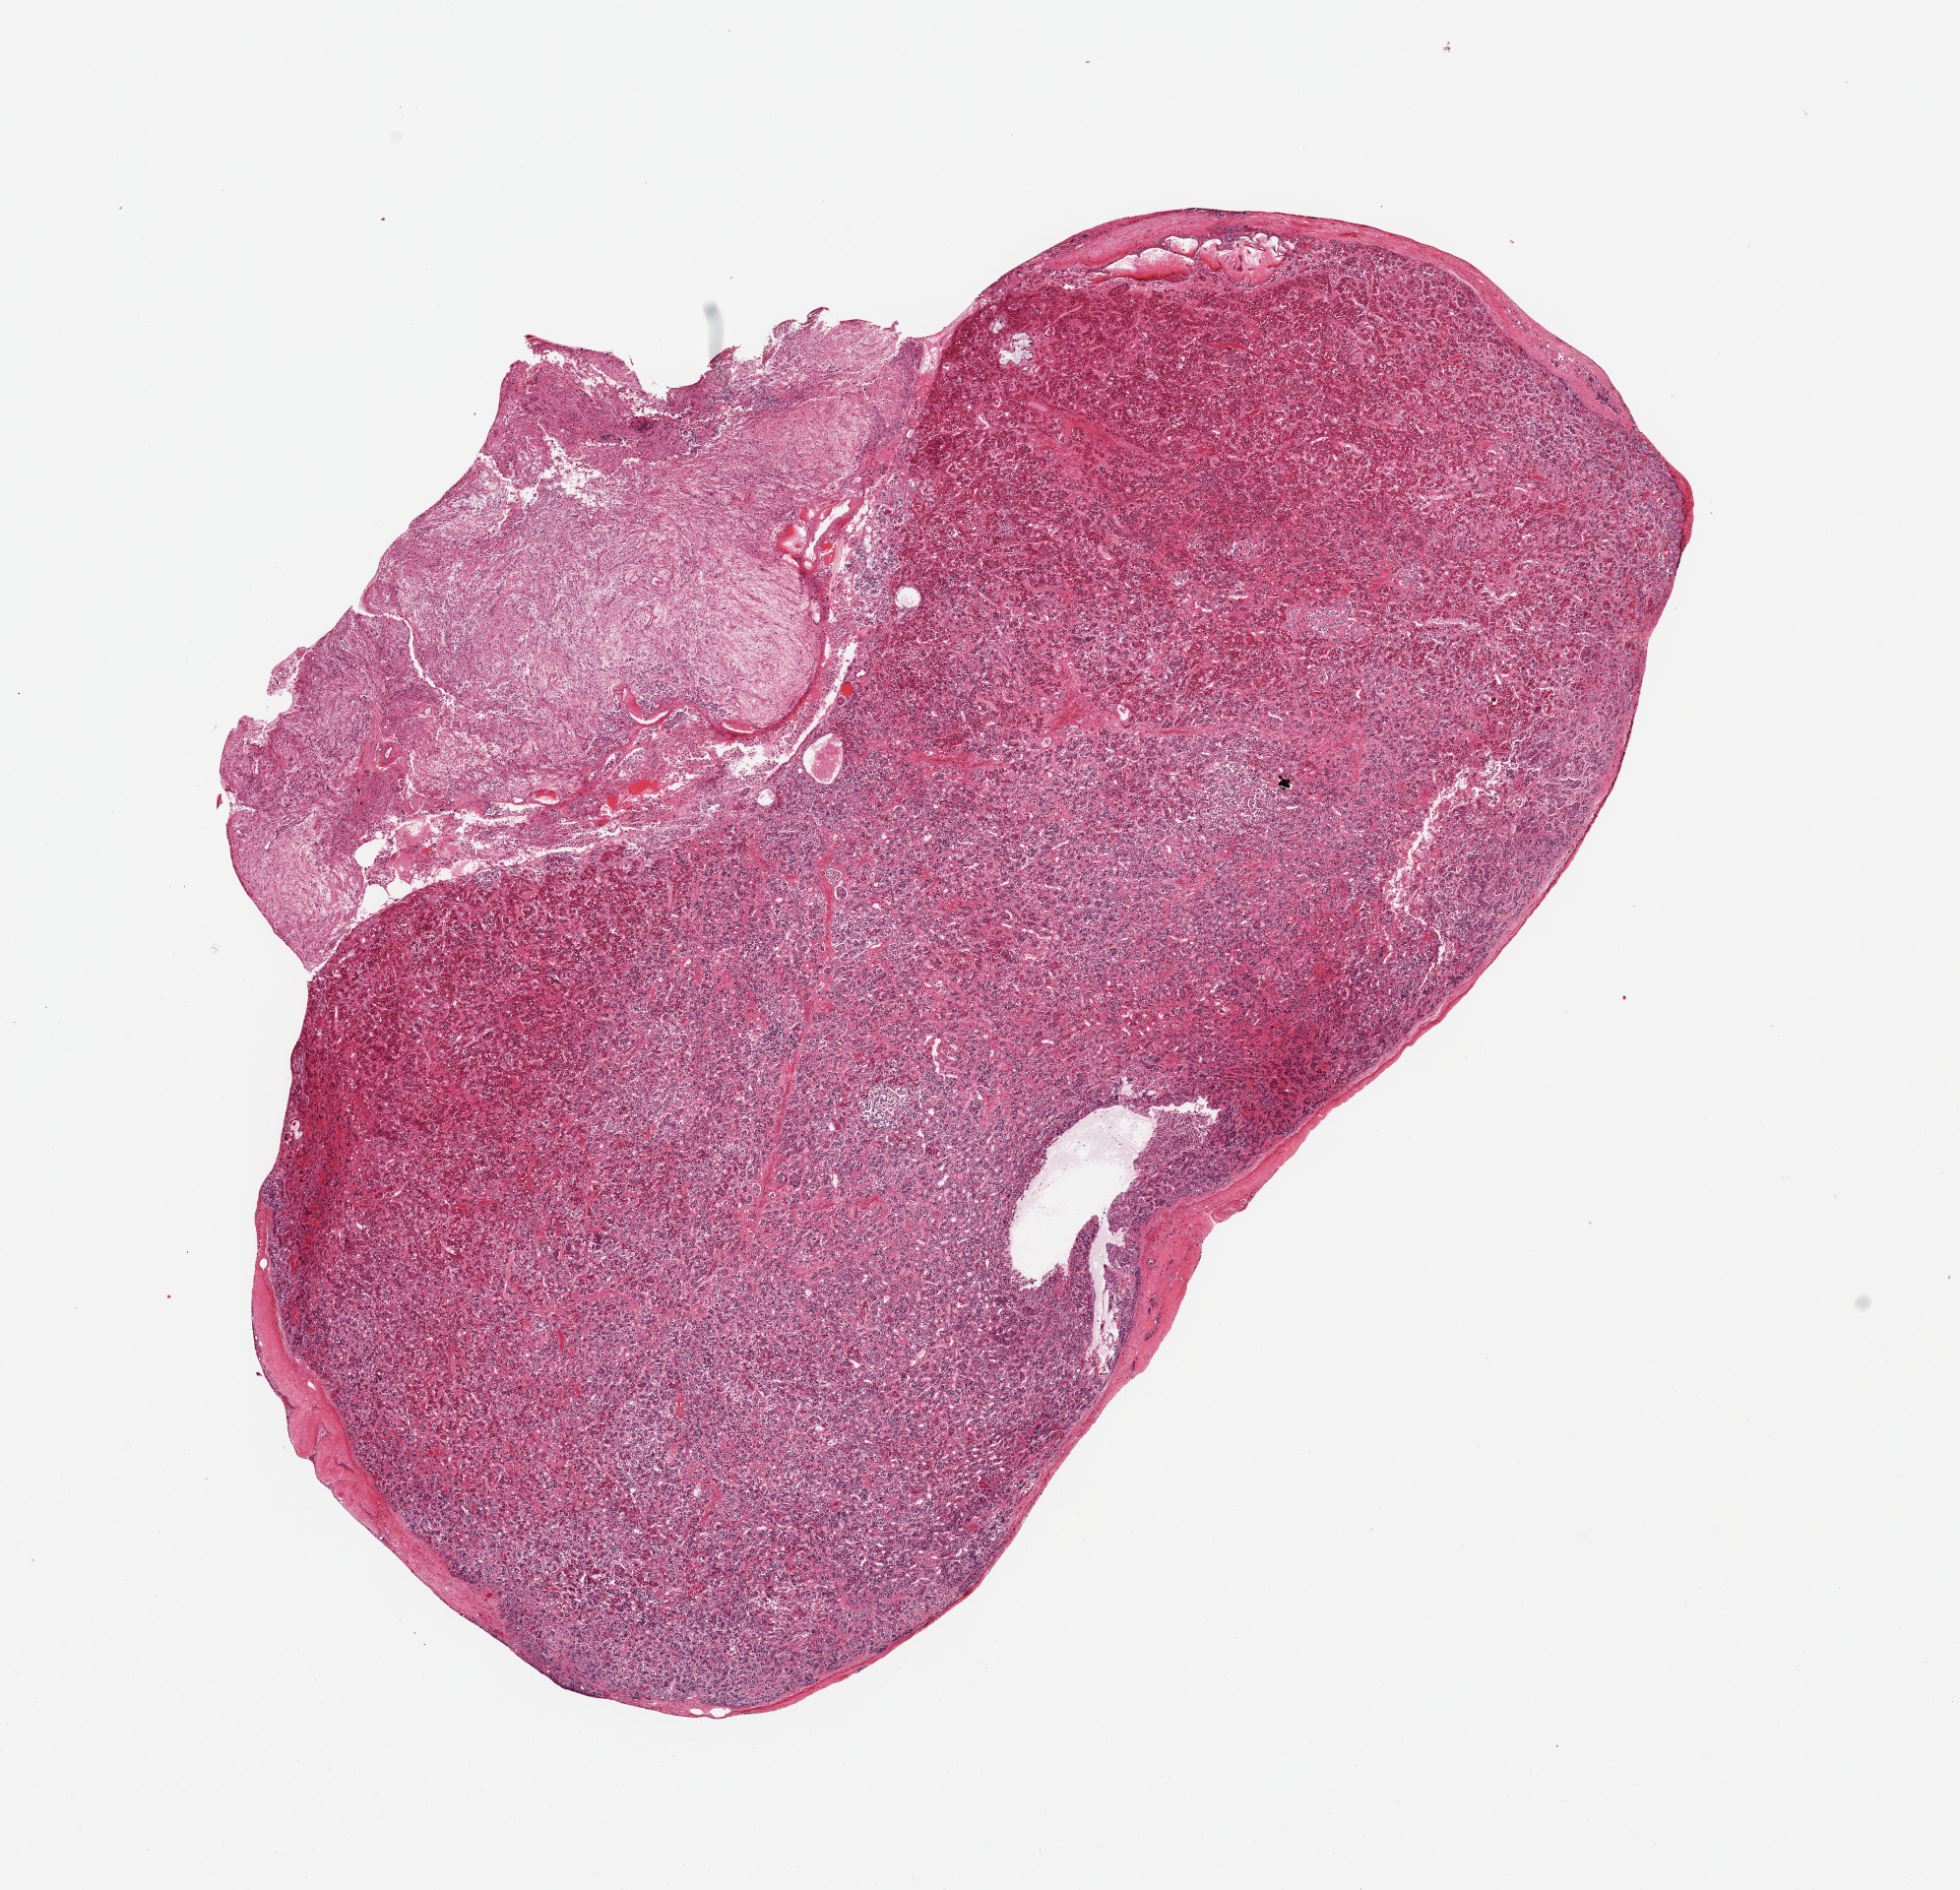
Digitized H&E-stained section, low-resolution overview of the scanned area, about 15.8 x 15.2 mm, PAXgene-fixed paraffin-embedded (PFPE) section, section of pituitary (target tissue), donor tissue sample. Donor sex: male.
Reviewer comment on this tissue sample: 1 piece; adenohypophysis and neurohypophysis.